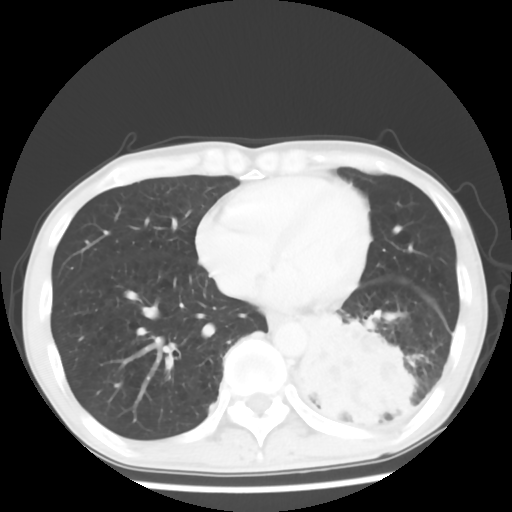
Chest CT, one axial slice. Slice 21 of 64 in the series (ordered by position). Lung window (W 1500 / L -600 HU). 5 mm slice thickness. 512 × 512 image matrix, field of view 313 × 313 mm. Patient: male, 68 years. From the clinical record (not read from this slice): clinical TNM (as recorded): T4 N0 M0.
Annotated regions visible in this slice (bounding box drawn by a radiologist):
- lung tumour (recorded histology: squamous cell carcinoma): bounding box (x1, y1, x2, y2) in pixels: (279, 294, 427, 453)